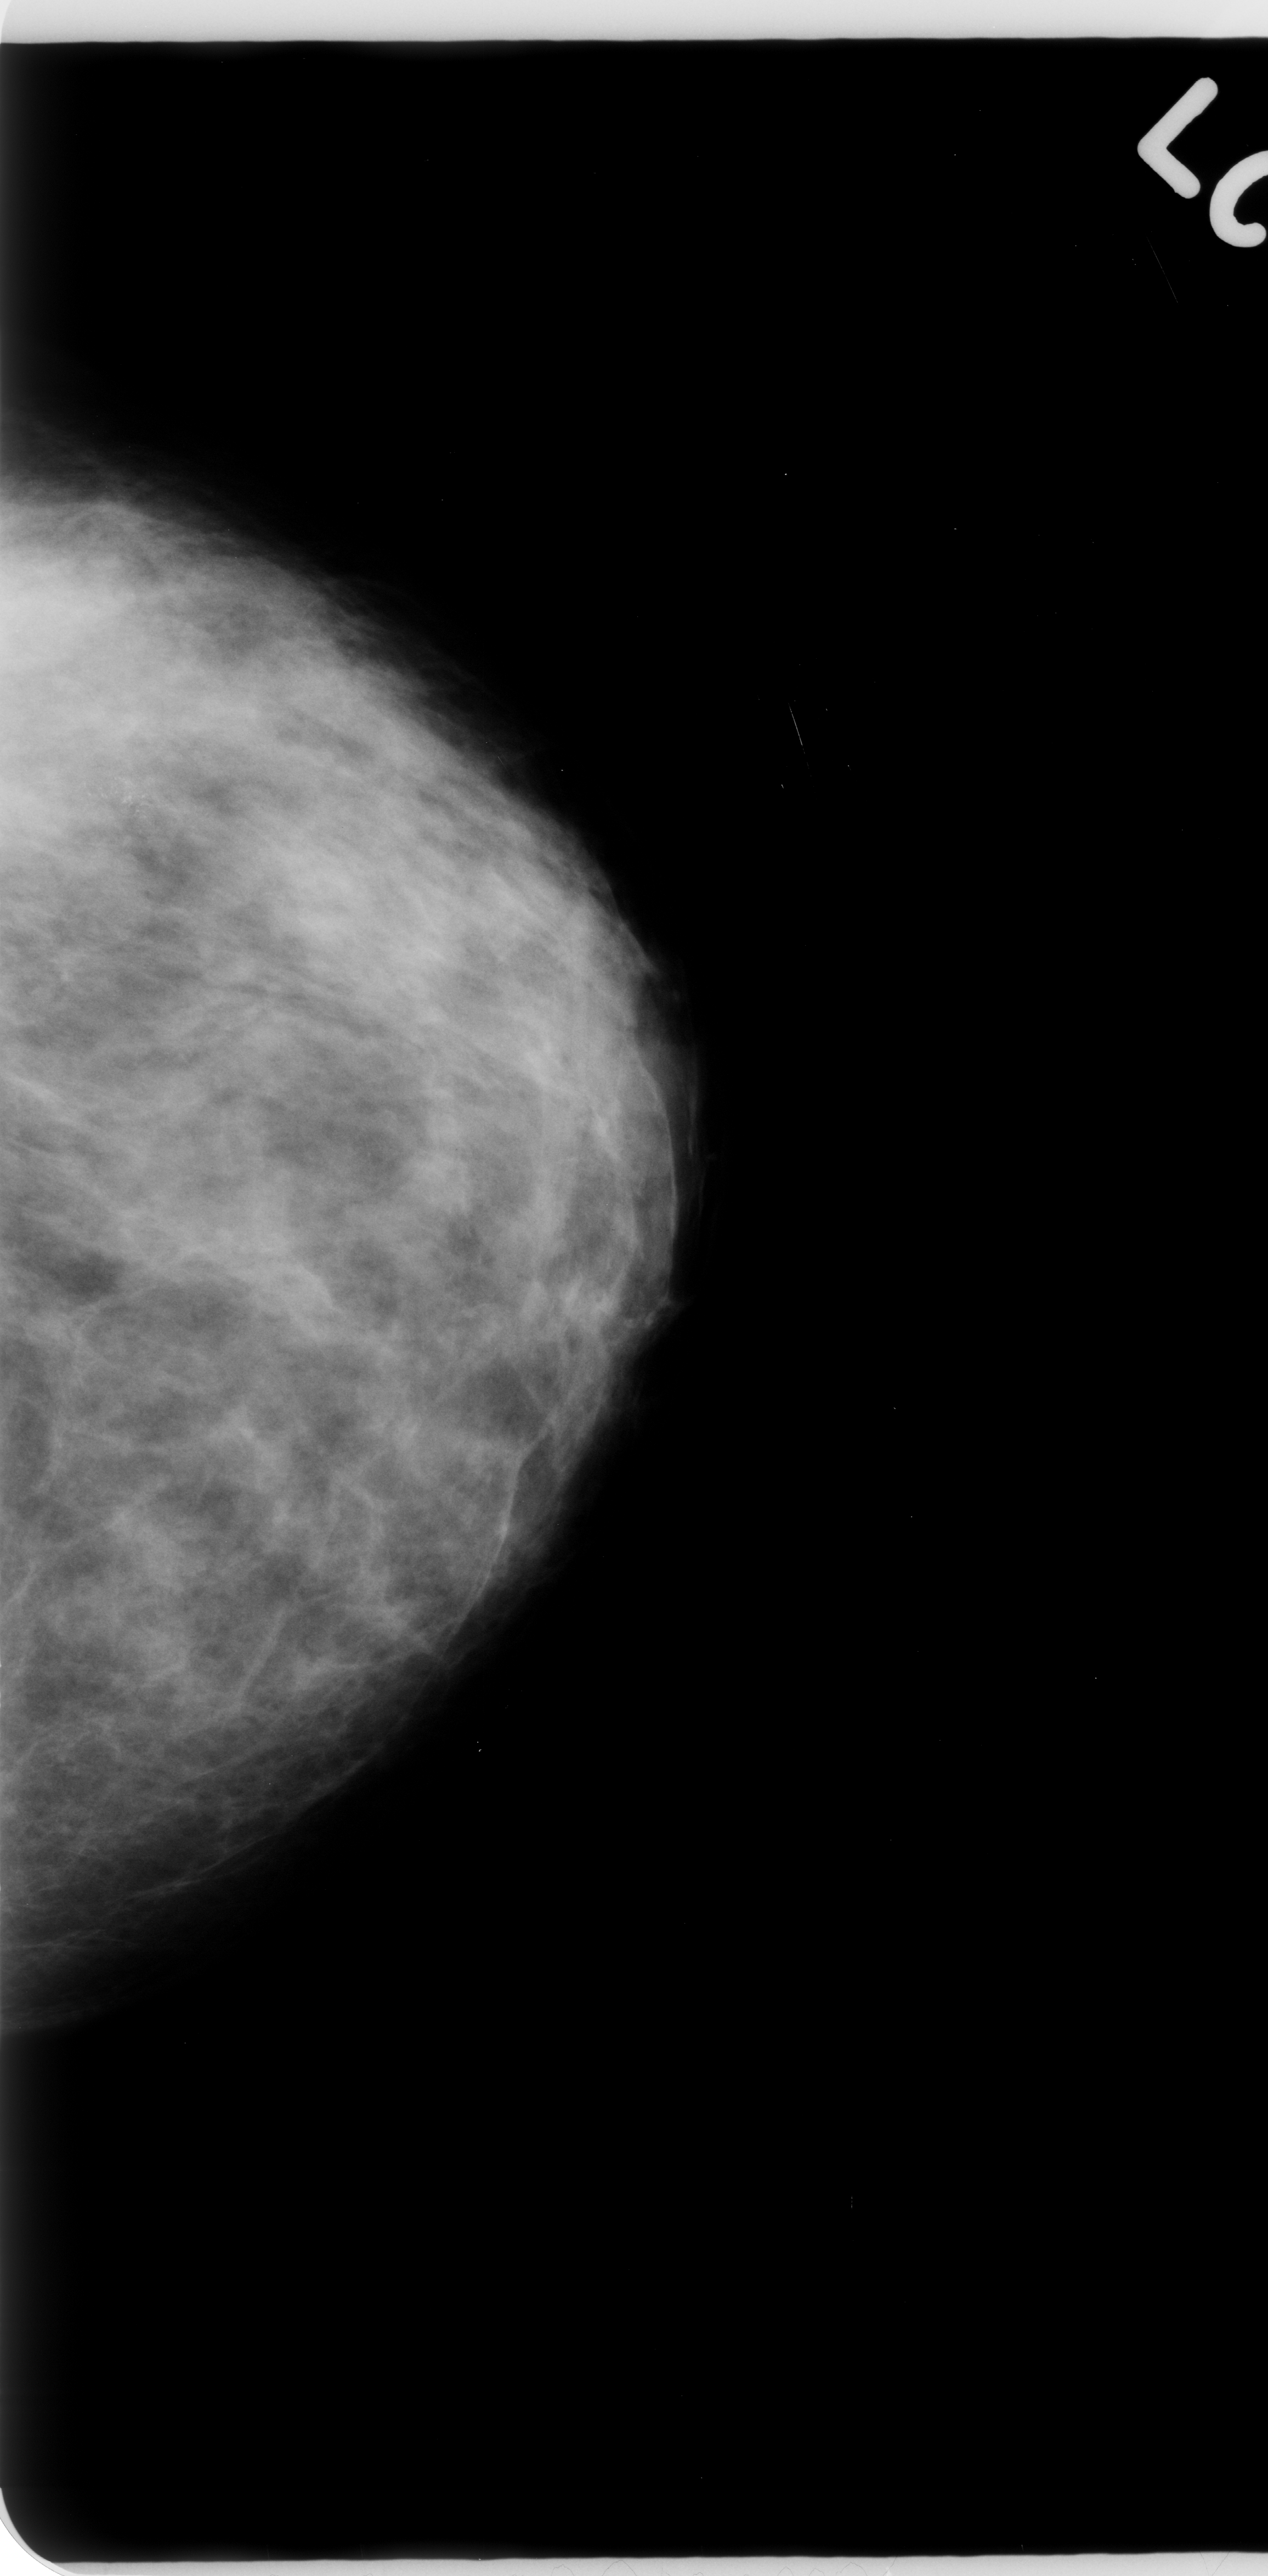
Scanned film-screen mammogram; left breast; CC view; breast composition: scattered fibroglandular densities (BI-RADS density category 2 of 4); 1268 × 2576 image matrix.
Marked abnormalities (boxes around the expert regions of interest):
- calcifications, morphology pleomorphic, distribution clustered; BI-RADS assessment category 5; pathology (as recorded): malignant: bounding box (x1, y1, x2, y2) in pixels: (21, 710, 304, 936)